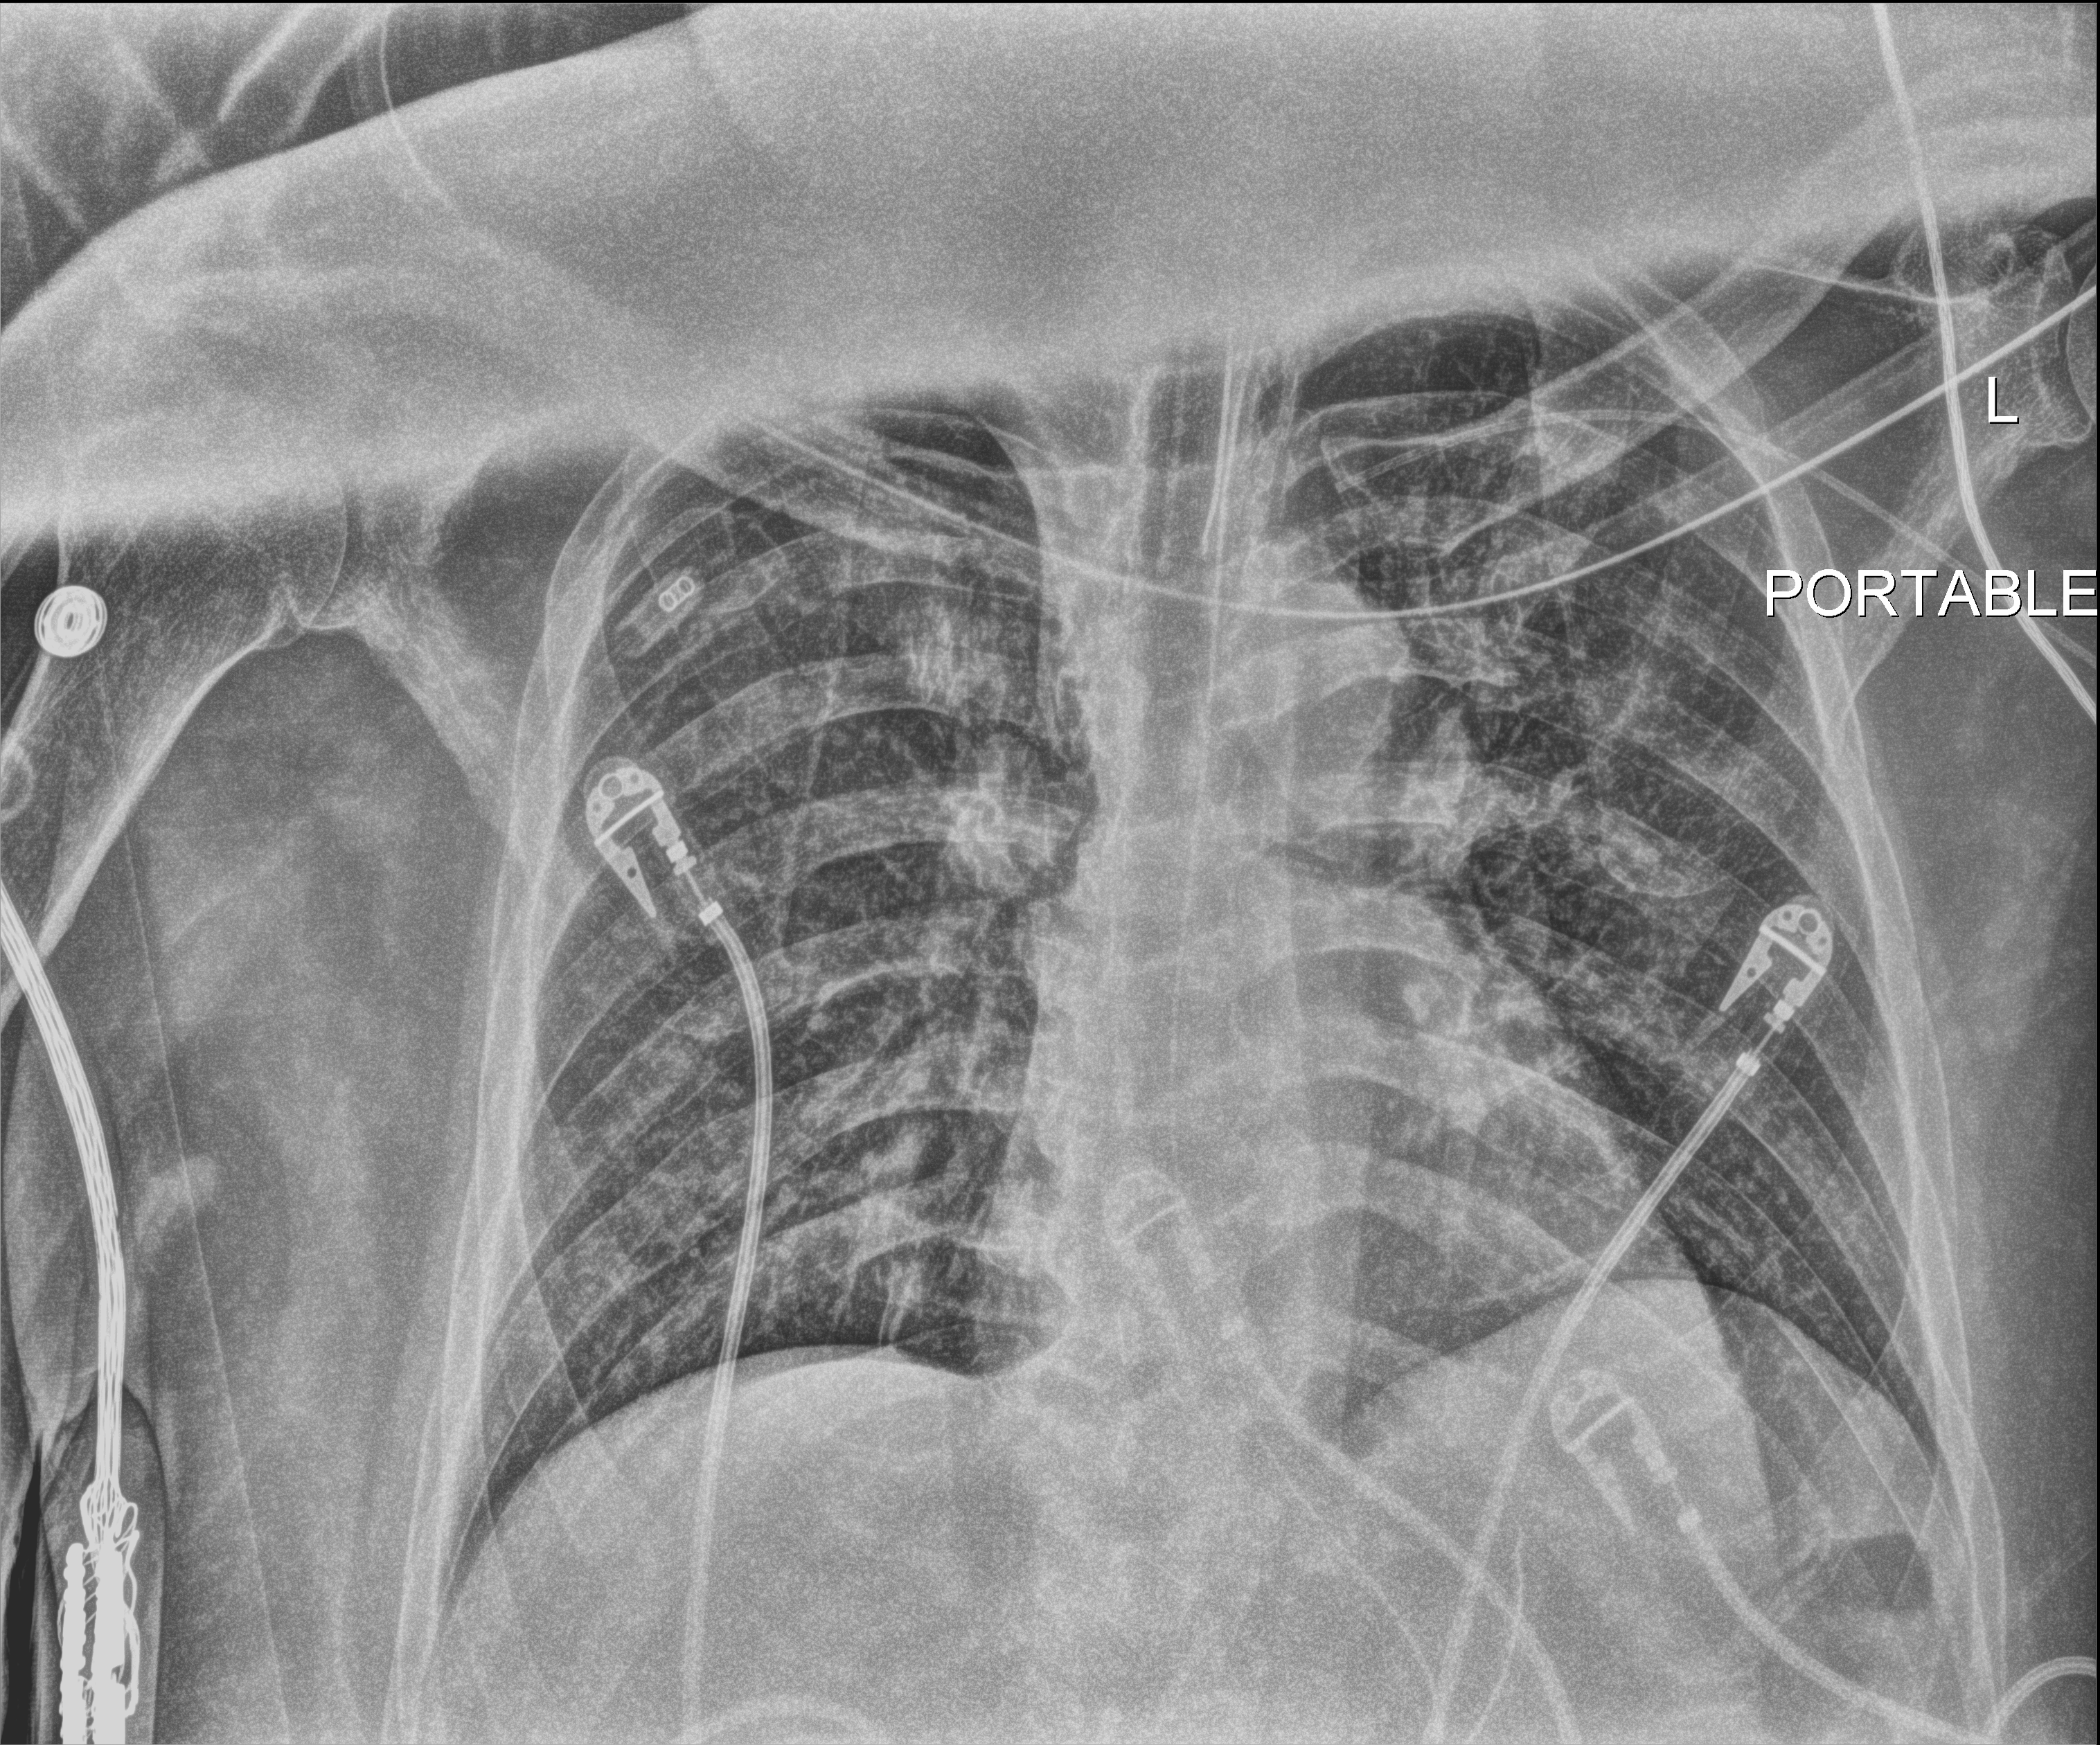
Portable chest radiograph; anteroposterior (AP) projection. Patient hospitalised with COVID-19, aged 18–59 years.
From the hospital-stay record, not from the radiograph (when in the stay this image was taken is not recorded): admitted to intensive care during this hospital stay: yes.